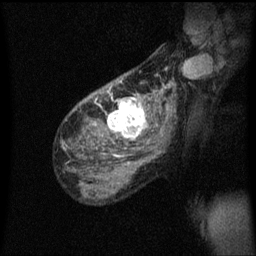
Breast MRI (dynamic contrast-enhanced), one sagittal slice. Slice 38 of 60 in the series (ordered by position). Dynamic contrast-enhanced series, image 2 of 3 at this slice position (ordered by acquisition). 1.5 T. TE 4.2 ms, TR 8.4 ms. 2 mm slice thickness. 256 × 256 image matrix, field of view 200 × 200 mm. Female patient, age 49 years.
Annotated regions visible in this slice (semi-automatically segmented with operator editing):
- analysis volume of interest (the breast-tissue region the enhancement analysis was run in; not a lesion): bounding box [x1, y1, x2, y2] px = [103, 90, 157, 151]
- tumour enhancement mask (voxels above the 70 % enhancement threshold inside the analysis volume of interest): [106, 90, 149, 141]